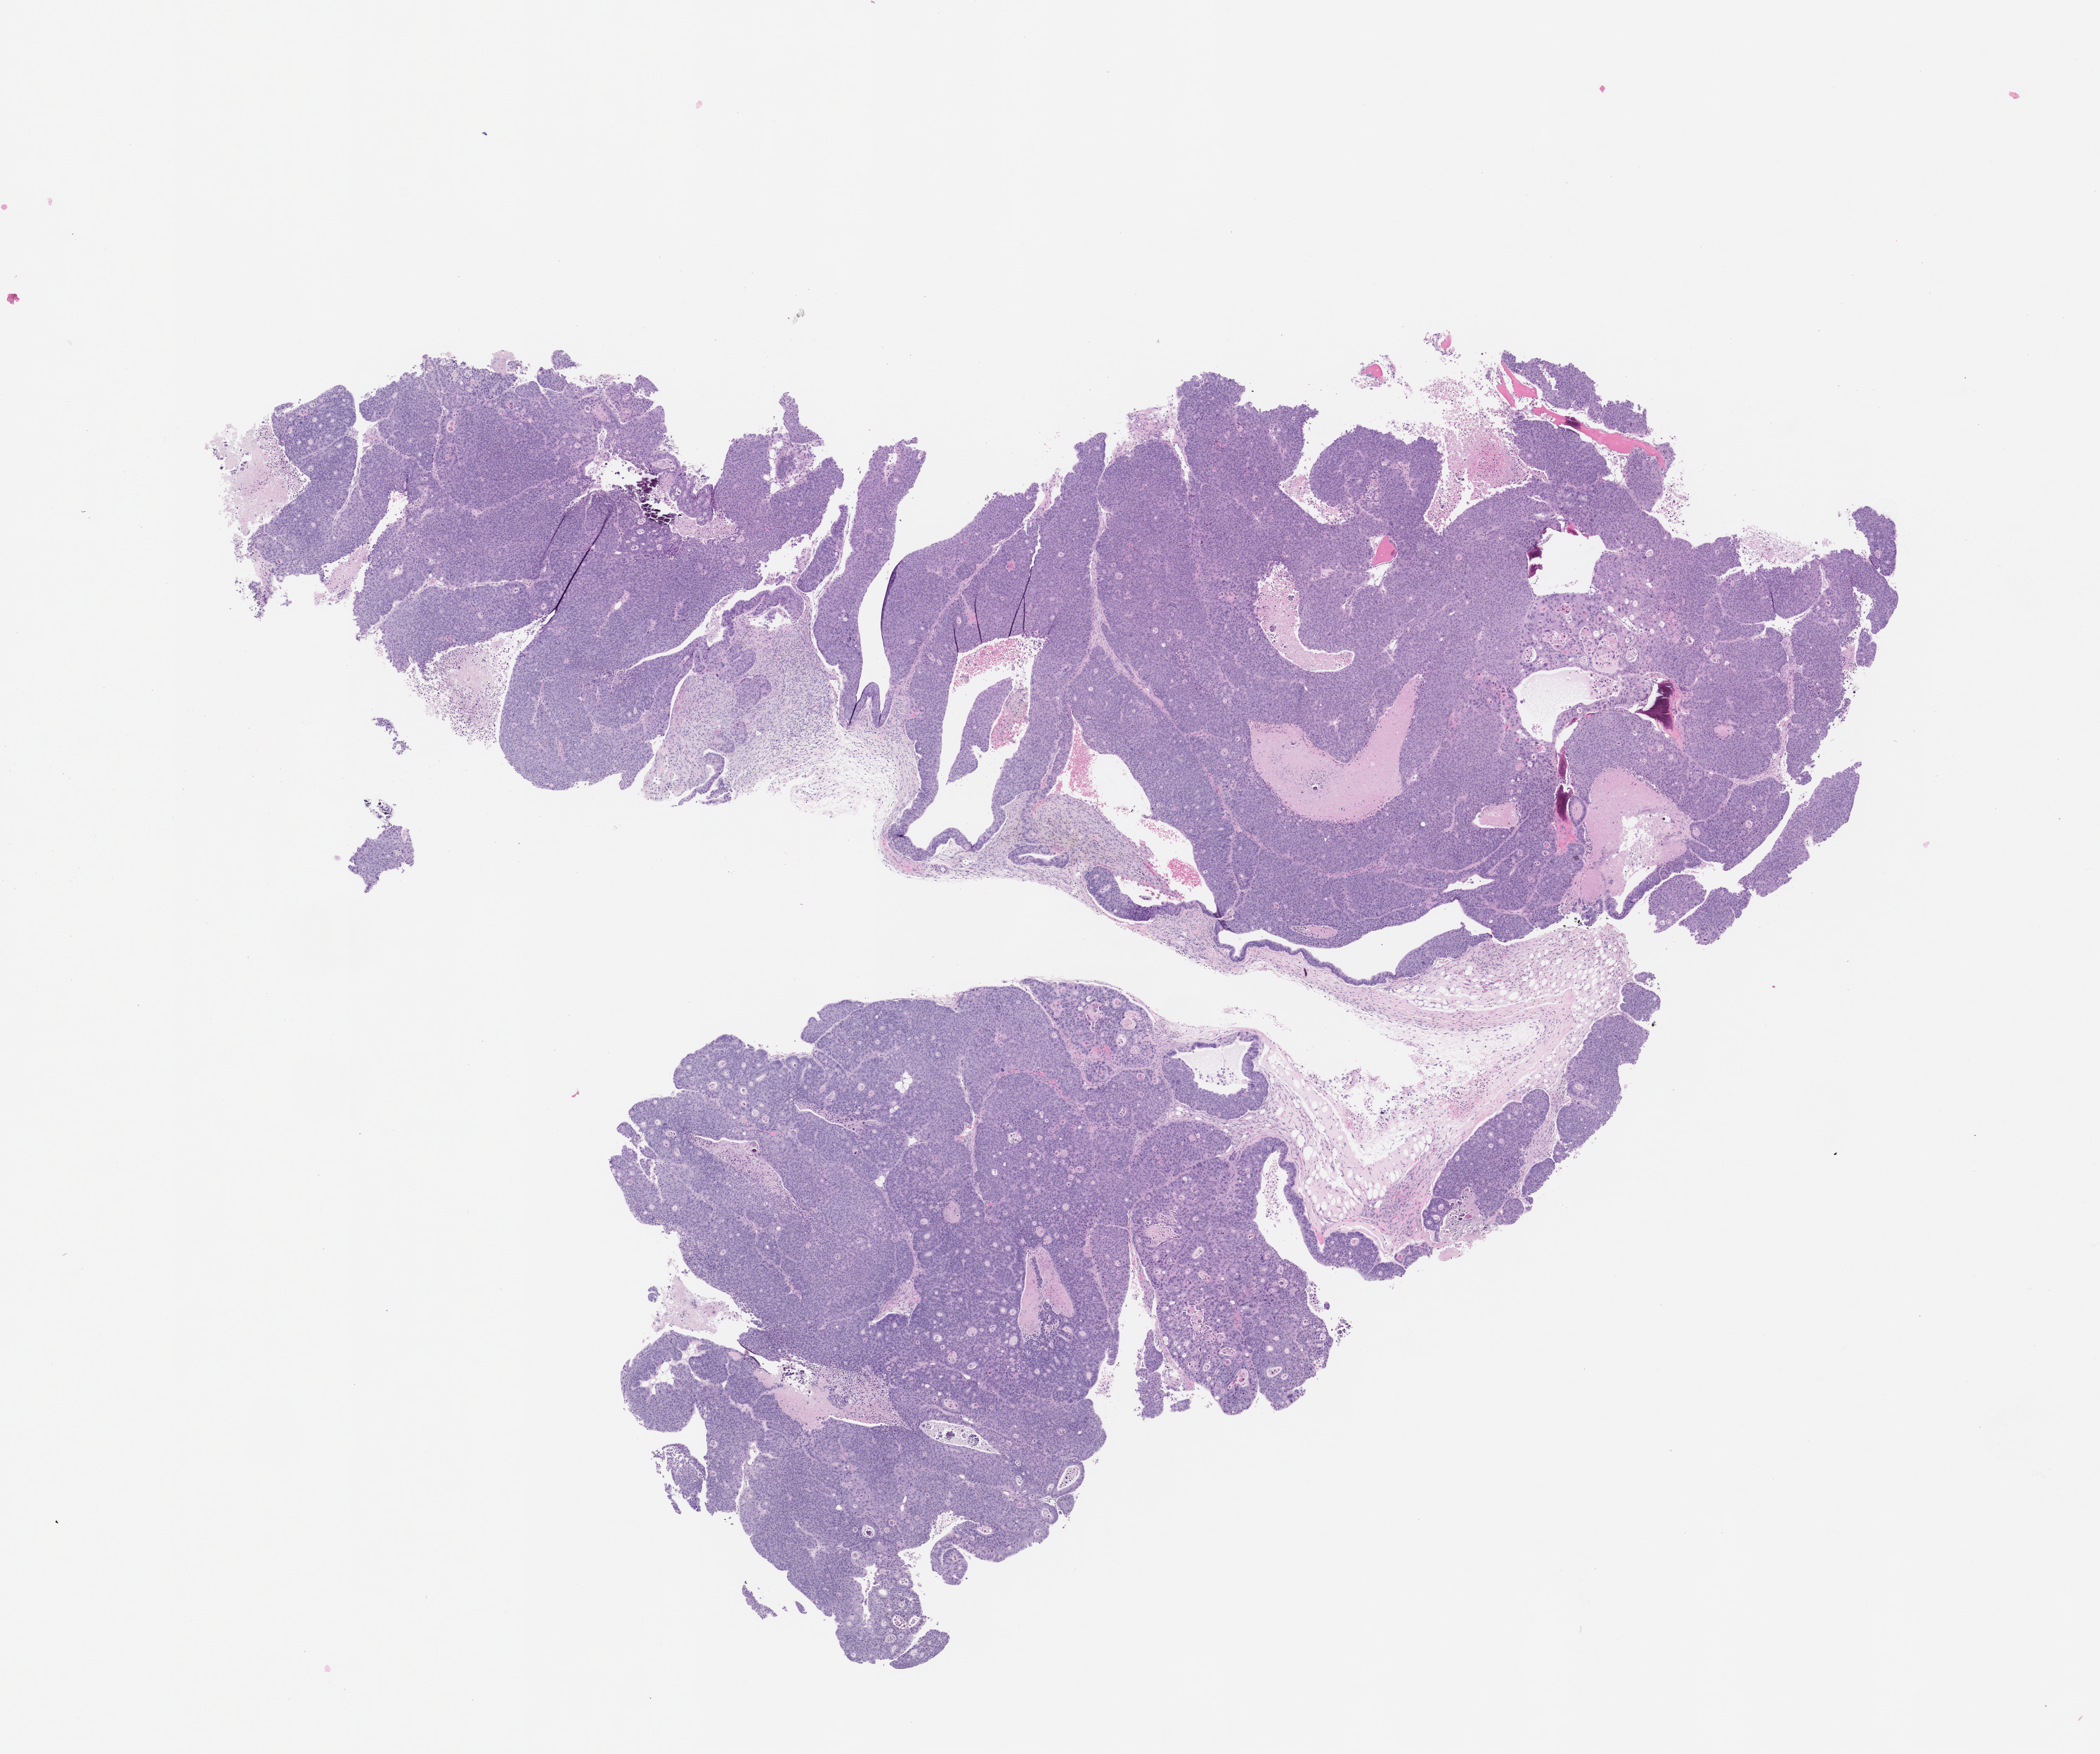
Whole-slide image, haematoxylin and eosin: patient-derived xenograft (human tumor grown in a mouse), passage 1, low-resolution overview of the scanned area, about 12.0 x 10.0 mm; formalin-fixed paraffin-embedded section; tumor site category: colon.
Originating patient diagnosis: Colon Adenocarcinoma.